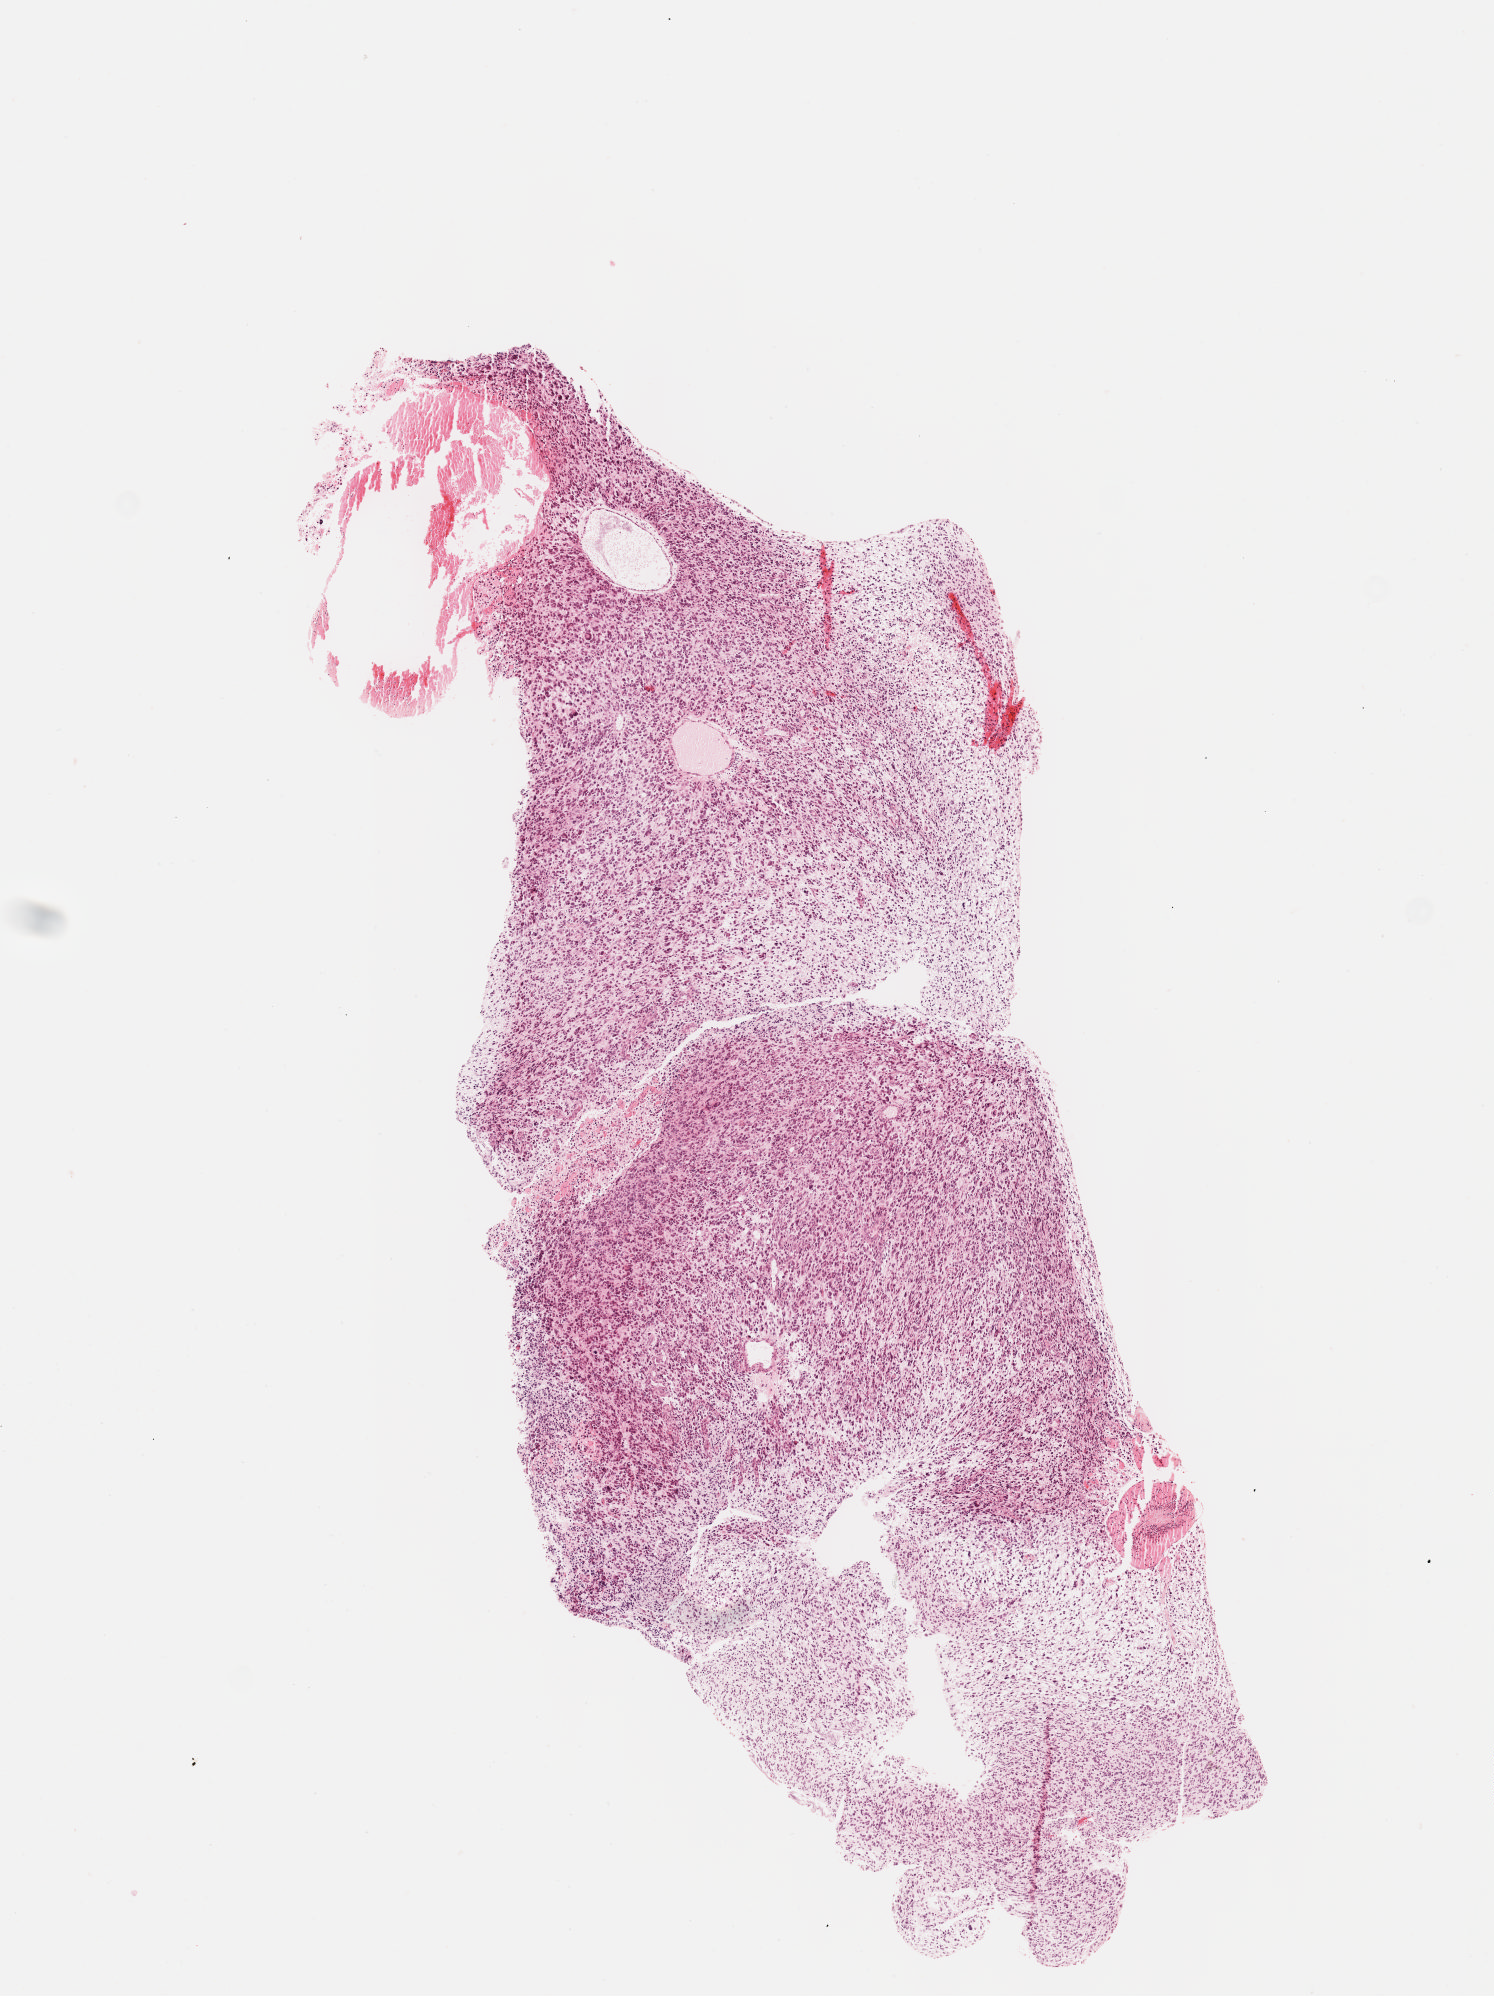
Digitized H&E tissue section (whole slide), low-resolution overview of the scanned area, about 6.0 x 8.1 mm, formalin-fixed paraffin-embedded (FFPE) diagnostic section, brain, primary tumour sample. Male, age 74 years at initial diagnosis.
Diagnosis: Glioblastoma.